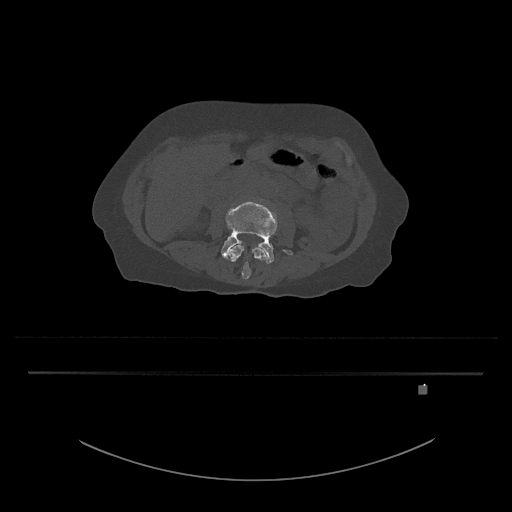
CT including the spine, one axial slice; slice 390 of 797 in the series (ordered by position); bone window (W 1800 / L 400 HU); 512 × 512 image matrix, field of view 500 × 500 mm. Female patient, age 57 years. Case-level facts recorded for this patient, not image findings: primary cancer: cervical.
Structures marked on this image (semi-automatically segmented with operator editing):
- L3 vertebra: bounding box (x1, y1, x2, y2) in pixels: (228, 244, 268, 280)
- L4 vertebra: (221, 201, 293, 264)